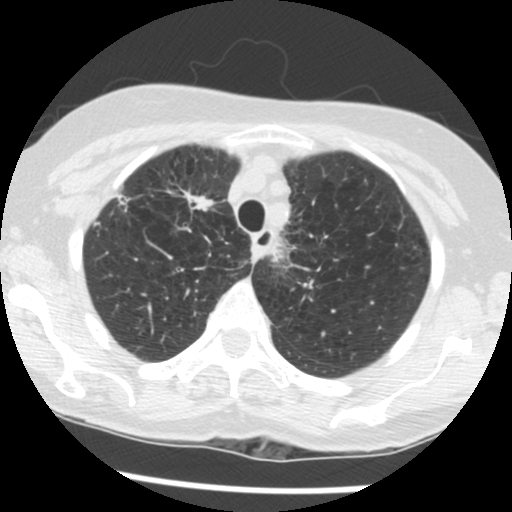
Low-dose screening chest CT, one axial slice; slice 100 of 124 in the series (ordered by position); 120 kVp; lung window (W 1500 / L -600 HU); 512 × 512 image matrix, field of view 290 × 290 mm.
Outlined on this slice (outlined manually by an expert reader):
- lesion 1 (tumor, upper lobe of right lung): bounding box [x1, y1, x2, y2] px = [183, 191, 214, 211]